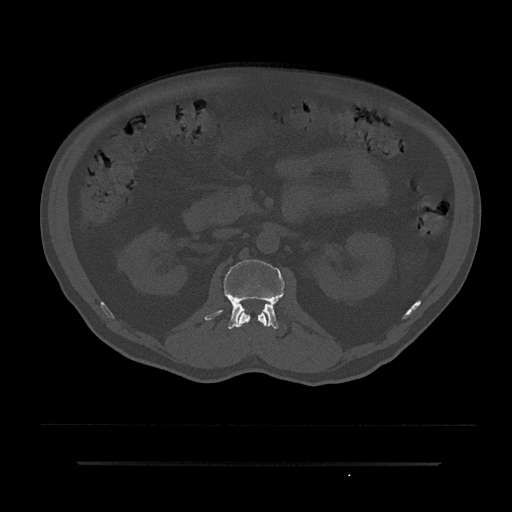
CT including the spine, one axial slice; slice 99 of 797 in the series (ordered by position); reconstruction kernel Br40s/3; bone window (W 1800 / L 400 HU); 0.5 mm slice thickness; 512 × 512 image matrix. Patient: male, 59 years. Case-level facts recorded for this patient, not image findings: primary cancer: bile ducts.
Outlined on this slice (semi-automatic segmentation, software-assisted and operator-edited):
- L1 vertebra: bounding box (x1, y1, x2, y2) in pixels: (237, 311, 268, 327)
- L2 vertebra: (205, 259, 285, 329)